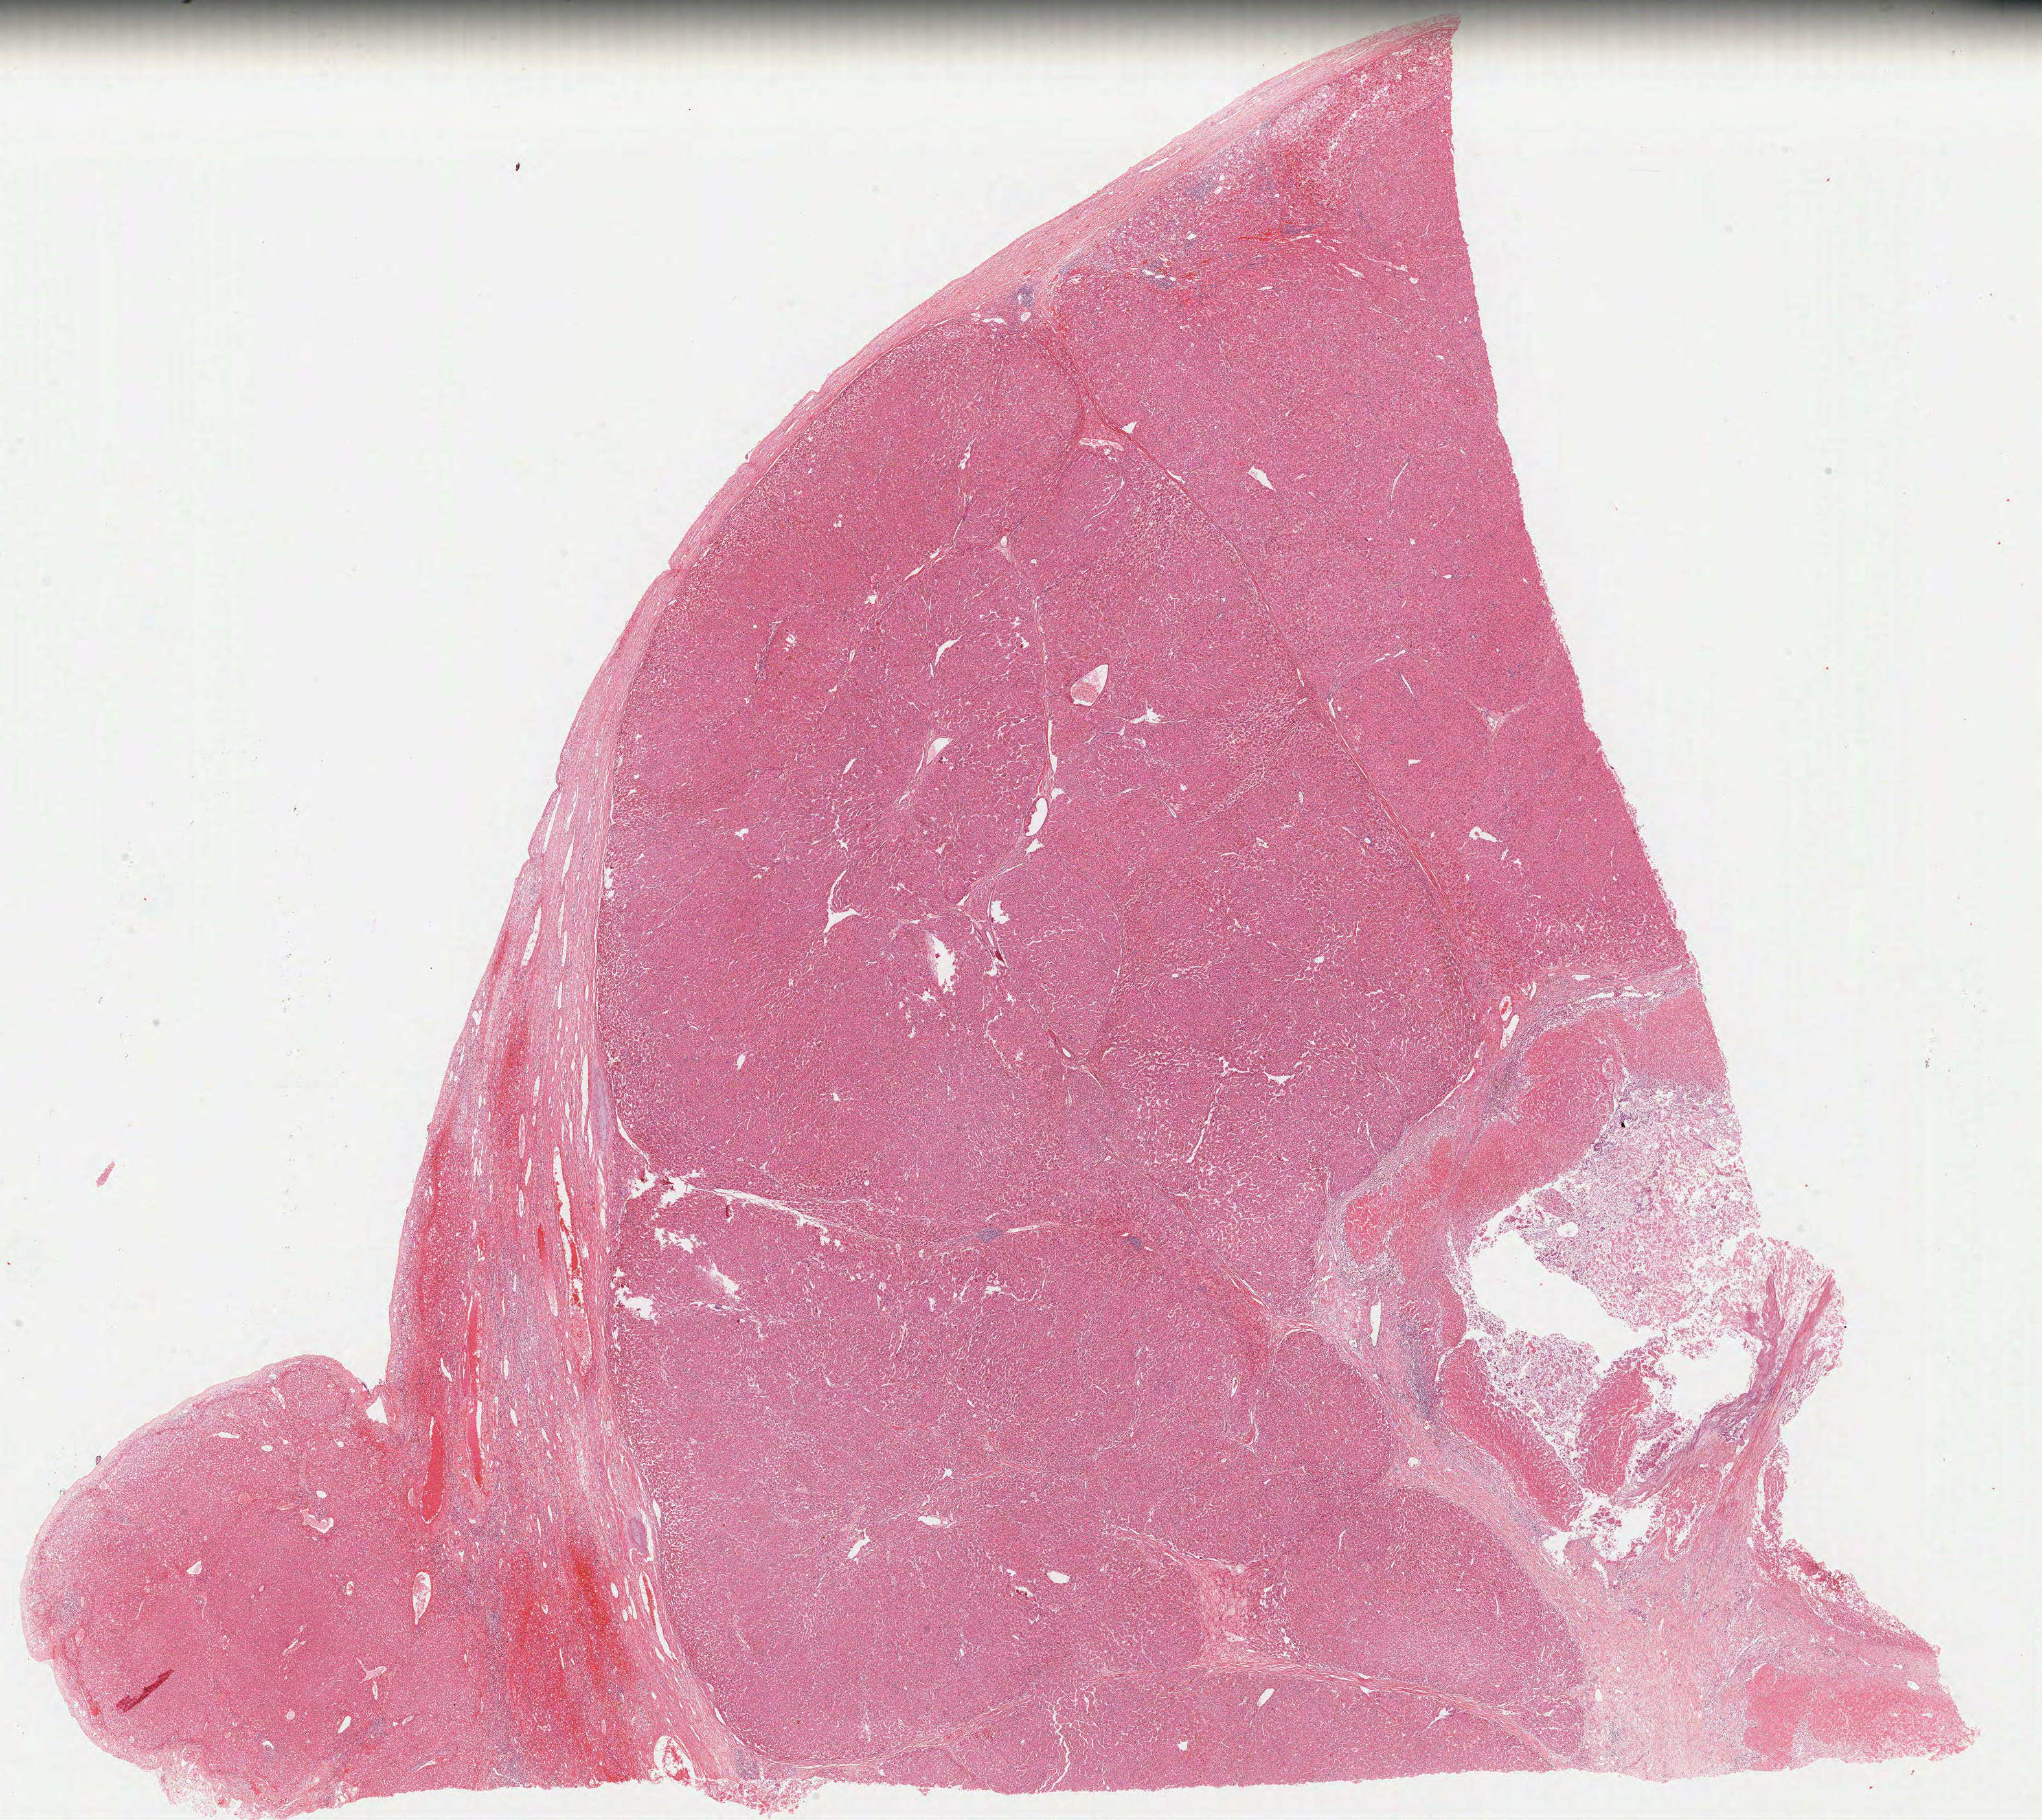
Digitized H&E tissue section (whole slide), shown as a low-resolution overview of the whole scanned area (about 24.9 x 22.2 mm, from a 40x scan). FFPE section. Sample: primary tumour, liver. Patient: male, age at initial diagnosis 48 years. Histologic grade: G1 (well differentiated).
Diagnosis: Hepatocellular carcinoma, NOS. TNM: T1 N0 M0. AJCC pathologic stage: I.